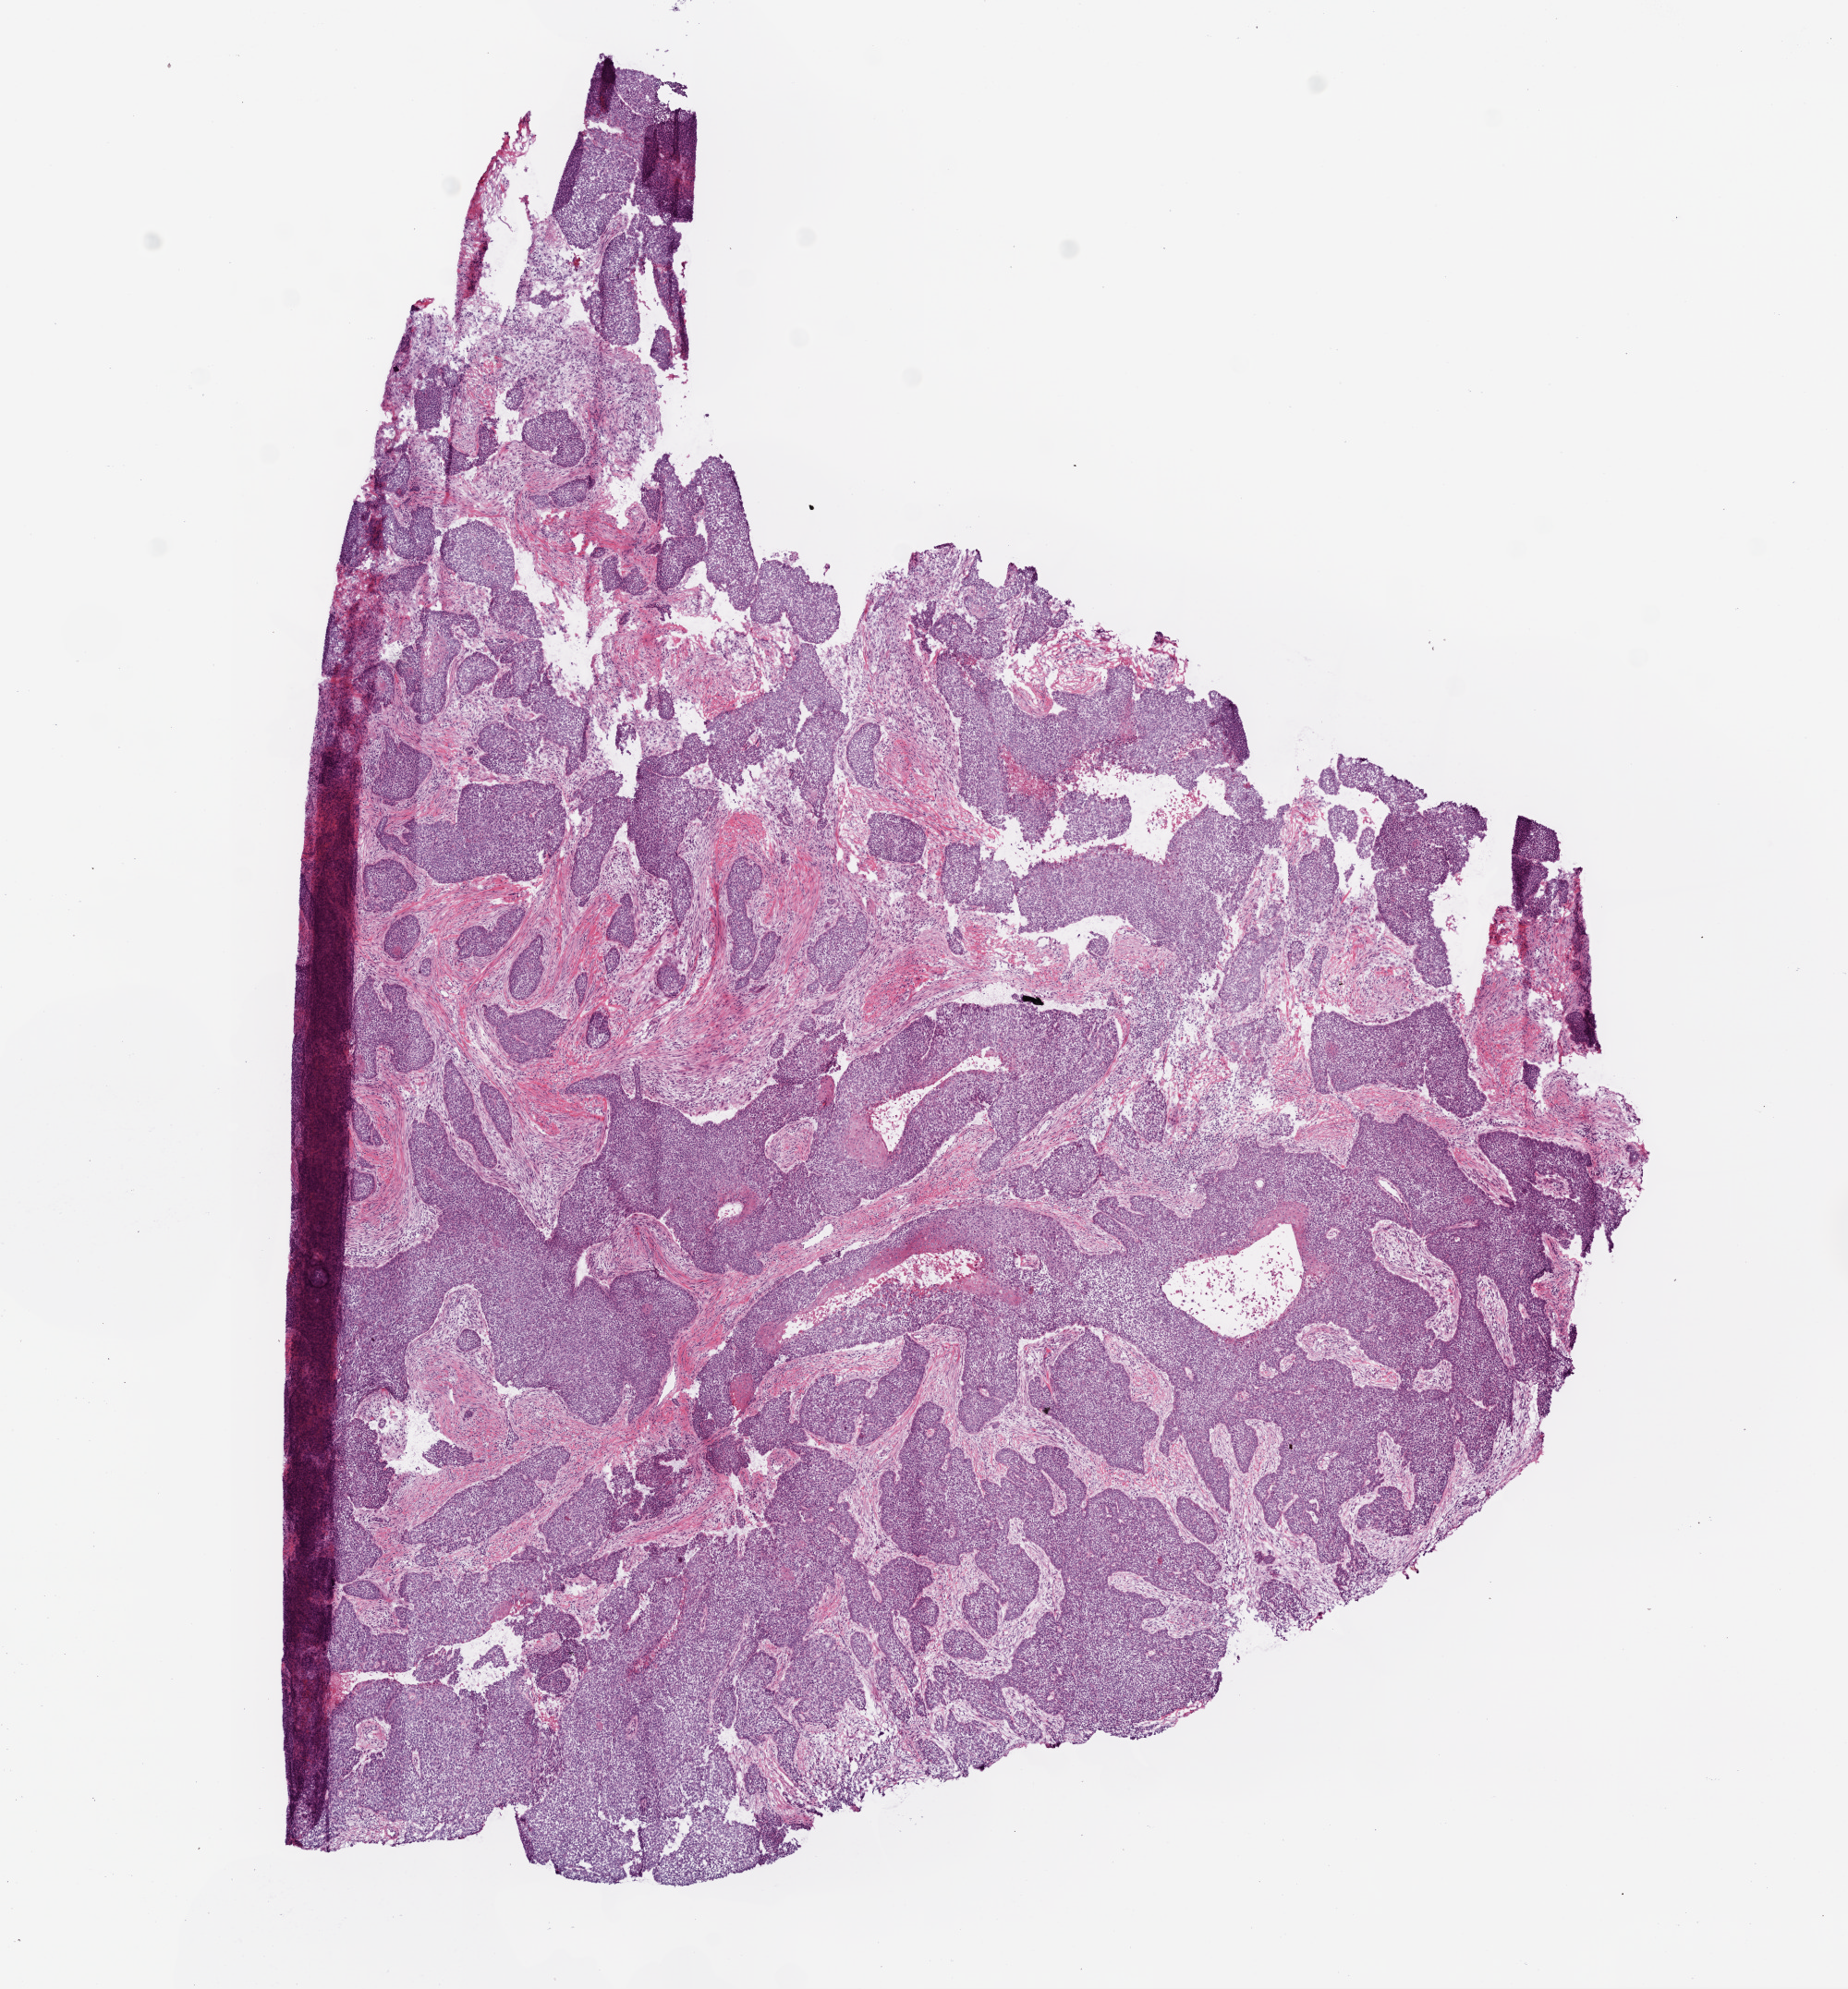
Whole-slide histology image, Hematoxylin and eosin (H&E) stained — shown as a low-resolution overview of the whole scanned area (about 8.0 x 8.6 mm); frozen section from the top of the tissue portion; primary tumour sample from the head and neck. Male, age 83 years at initial diagnosis. Composition of this section per pathologist review: tumour cells 85%, tumour nuclei 80%.
Histologic diagnosis: Squamous cell carcinoma, NOS (larynx, NOS).